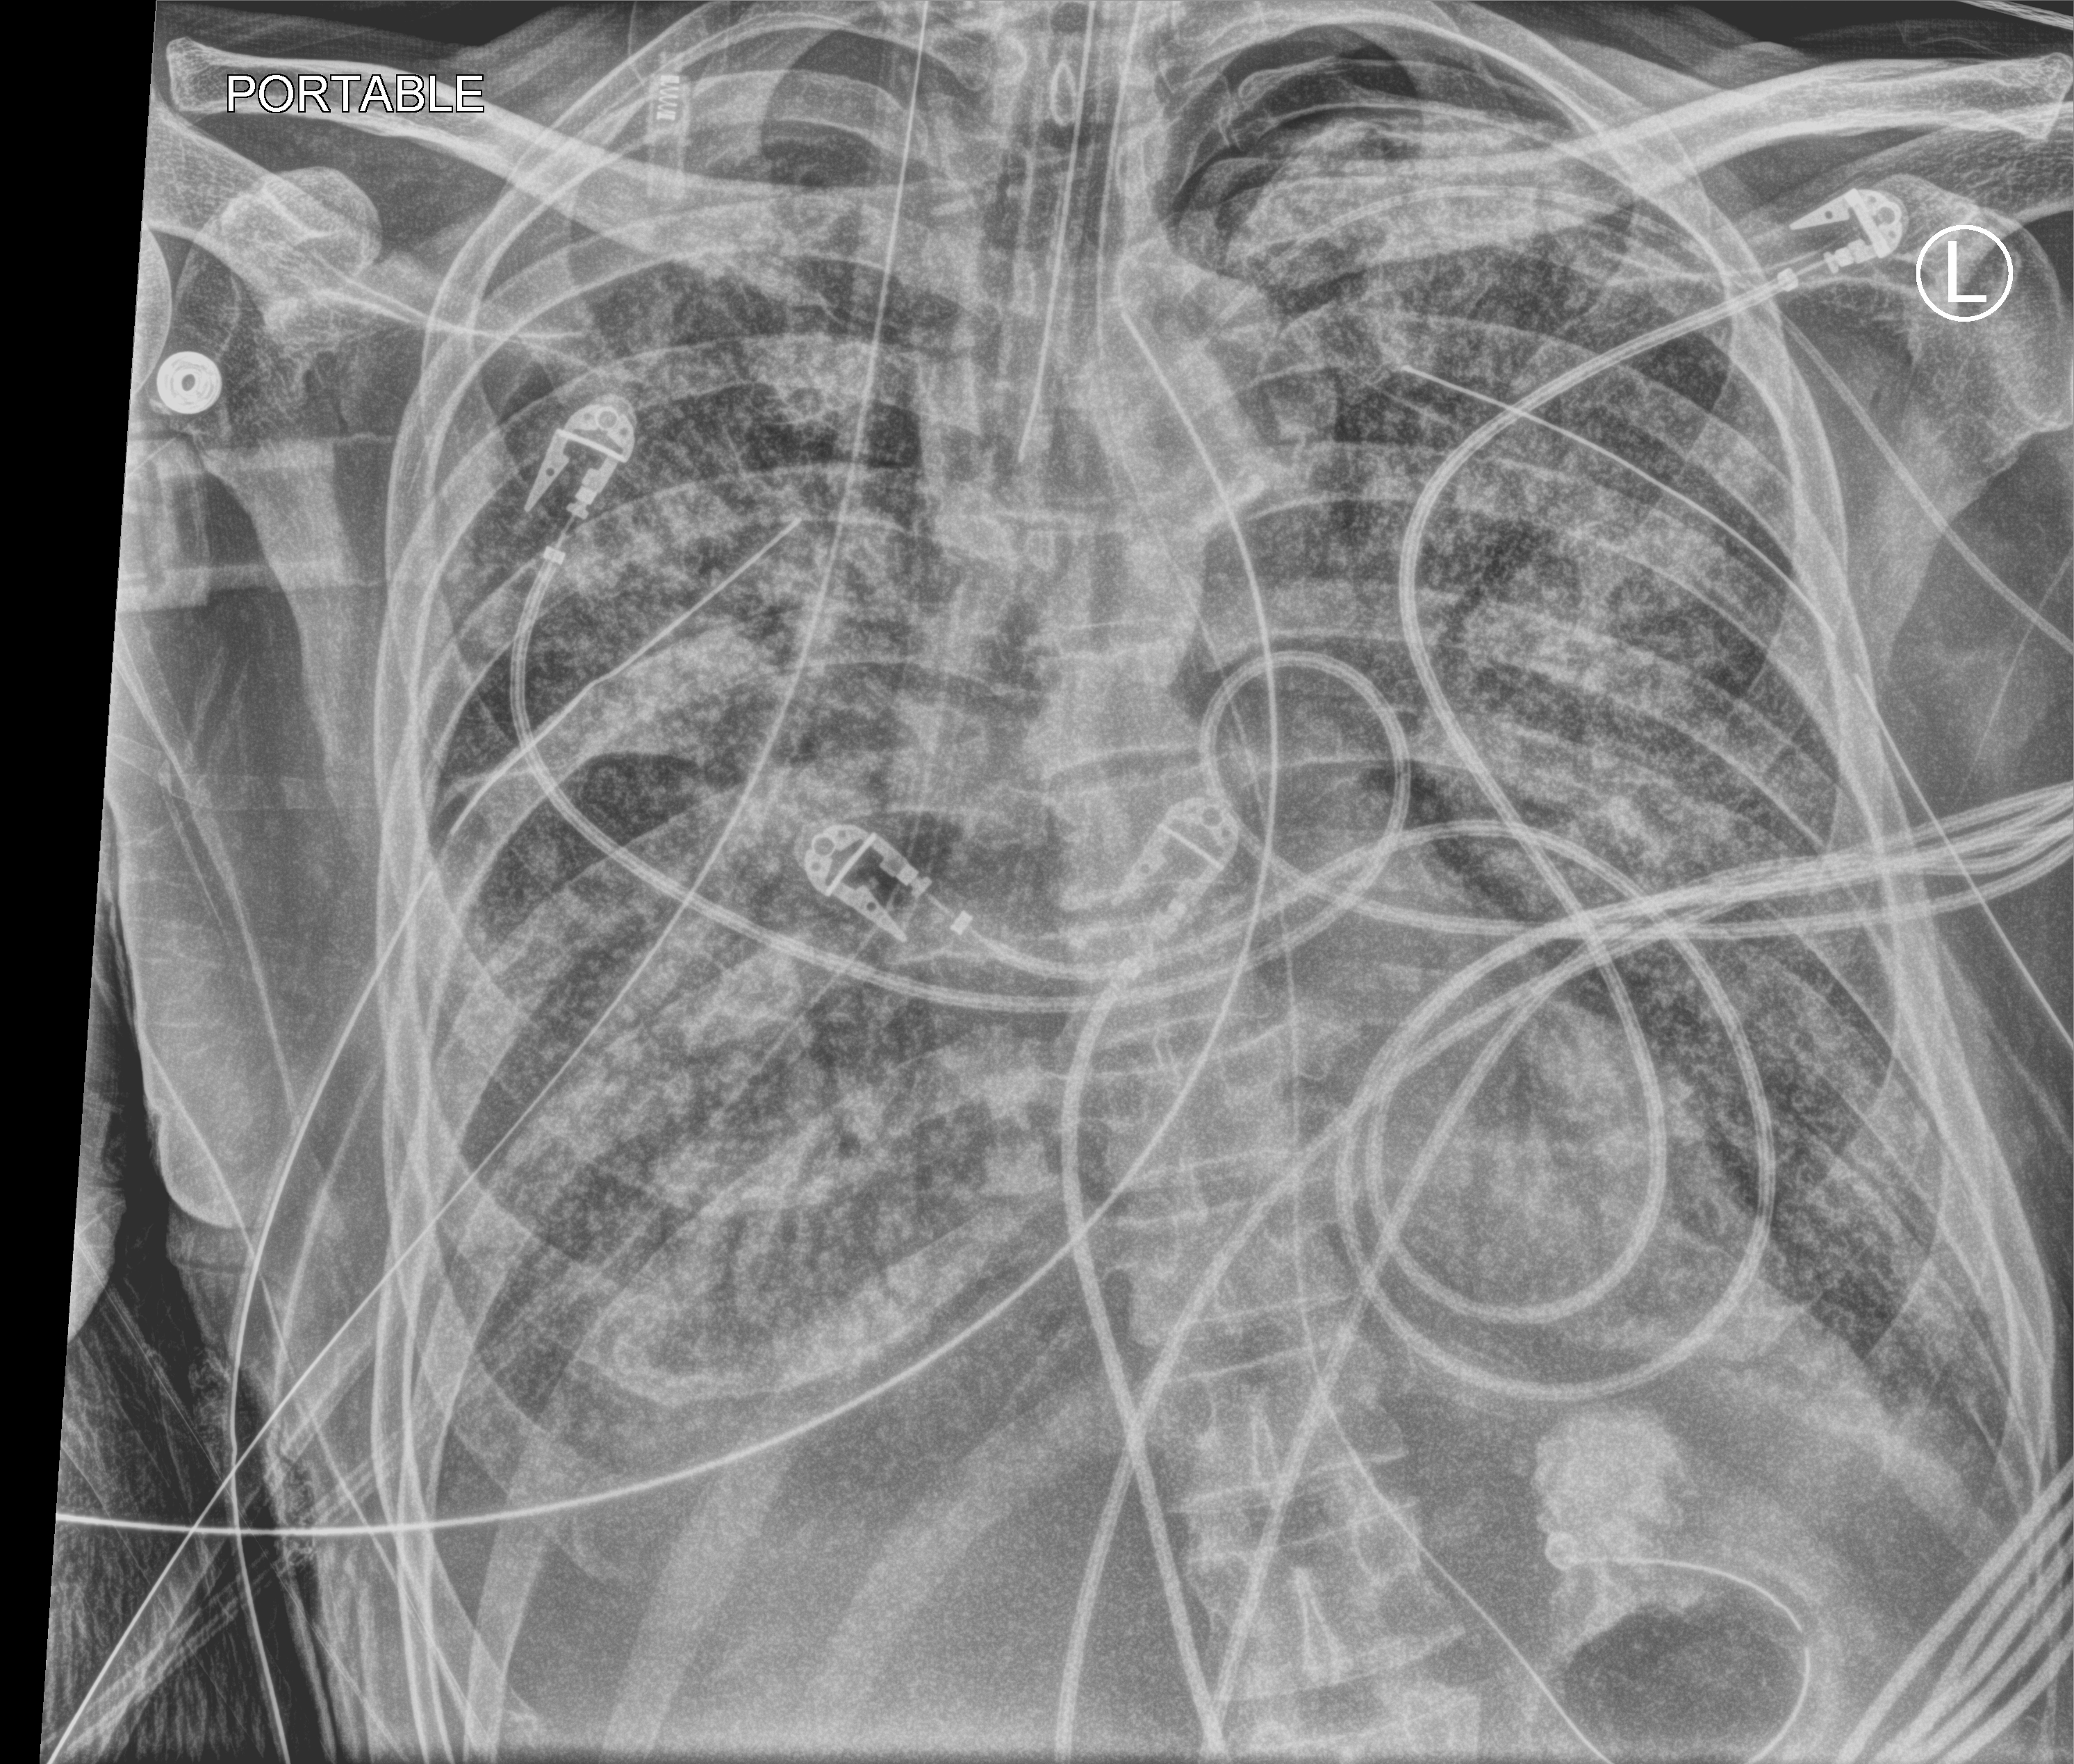
Chest X-ray (portable). Patient hospitalised with COVID-19; male, aged 60–74 years.
Admission-level facts for this patient (not findings on this image; timing relative to this image not recorded): admitted to intensive care during this hospital stay: yes.